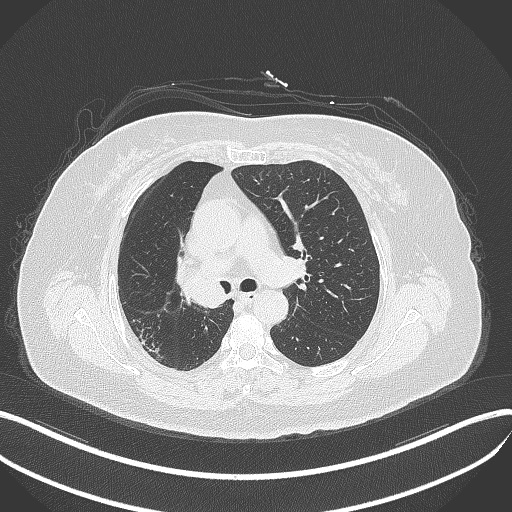
Chest CT, one axial slice. Reconstruction kernel B70f. Lung window (W 1500 / L -600 HU). 1 mm slice thickness. 512 × 512 image matrix. Patient: female, 60 years. From the clinical record (not read from this slice): clinical TNM (as recorded): T1c N0 M0; histopathological grade: G1-G2.
Structures marked on this image (bounding box drawn by a radiologist):
- lung tumour (recorded histology: squamous cell carcinoma): box from (x=175, y=257) to (x=230, y=308) px